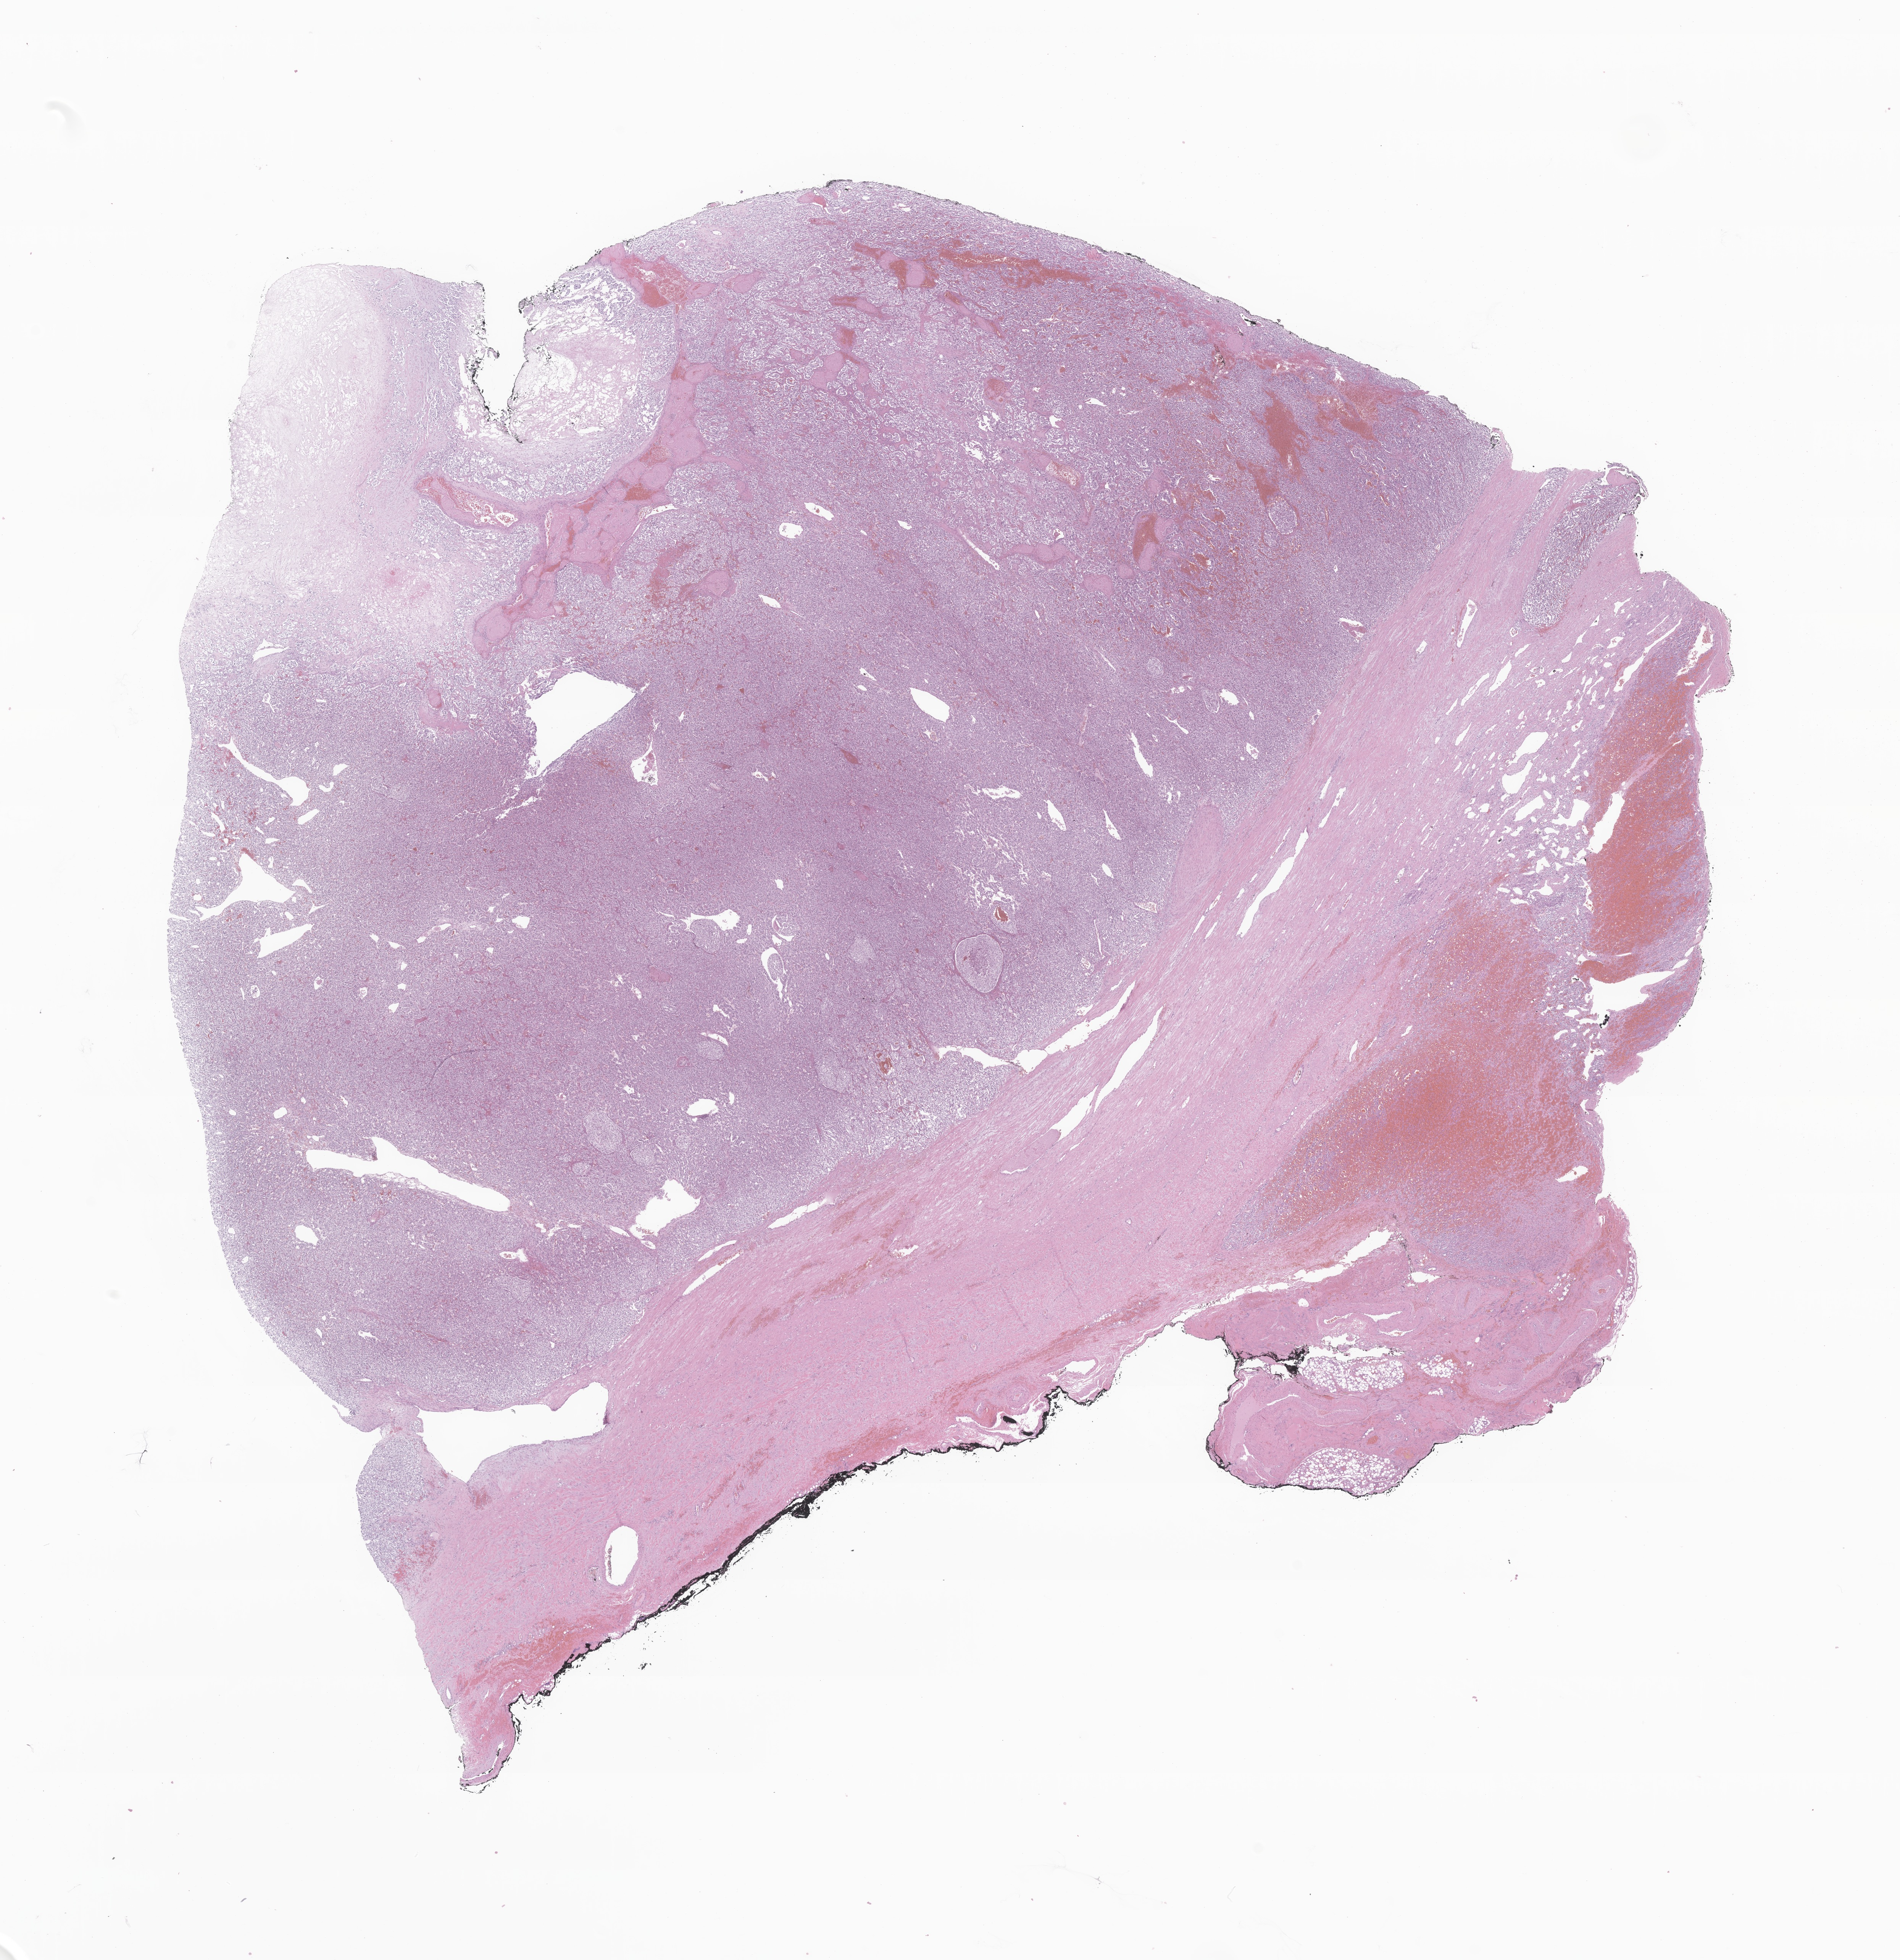
Digitized haematoxylin and eosin-stained section of tumor tissue from the kidney, shown as a low-resolution overview of the whole scanned area (about 21.0 x 21.7 mm); FFPE section. Patient male; age 177 months (14 years 9 months).
Diagnosis (ICD-O-3 morphology term): Pheochromocytoma, NOS.